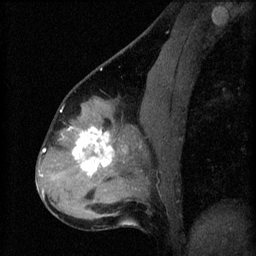
Breast MRI (dynamic contrast-enhanced), one sagittal slice; slice 29 of 60 in the series (ordered by position); 3 images stored at this slice position (order not interpretable as contrast timing); 1.5 T; TE 4.2 ms, TR 8.2 ms; 256 × 256 image matrix, field of view 180 × 180 mm. Female patient, age 37 years.
Outlined on this slice (semi-automatic segmentation, software-assisted and operator-edited):
- analysis volume of interest (the breast-tissue region the enhancement analysis was run in; not a lesion): bounding box (x1, y1, x2, y2) in pixels: (67, 120, 122, 179)
- tumour enhancement mask (voxels above the 70 % enhancement threshold inside the analysis volume of interest): (68, 126, 114, 177)